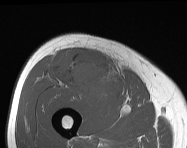
MRI of an extremity soft-tissue mass, one axial slice. Slice 71 of 114 in the series (ordered by position). MR volume resampled by the dataset authors to the PET/CT grid (not the native acquisition matrix). 187 × 148 image matrix, field of view 183 × 145 mm. Male patient. From the clinical record (not read from this slice): histological type: pleiomorphic leiomyosarcoma; grade: intermediate; site of the primary tumour: right thigh.
Annotated regions visible in this slice (expert contour drawn on MRI and transferred to this co-registered scan by the dataset authors):
- gross tumour volume including surrounding oedema: bounding box (x1, y1, x2, y2) in pixels: (56, 49, 112, 94)
- gross tumour volume (mass): (61, 52, 110, 92)